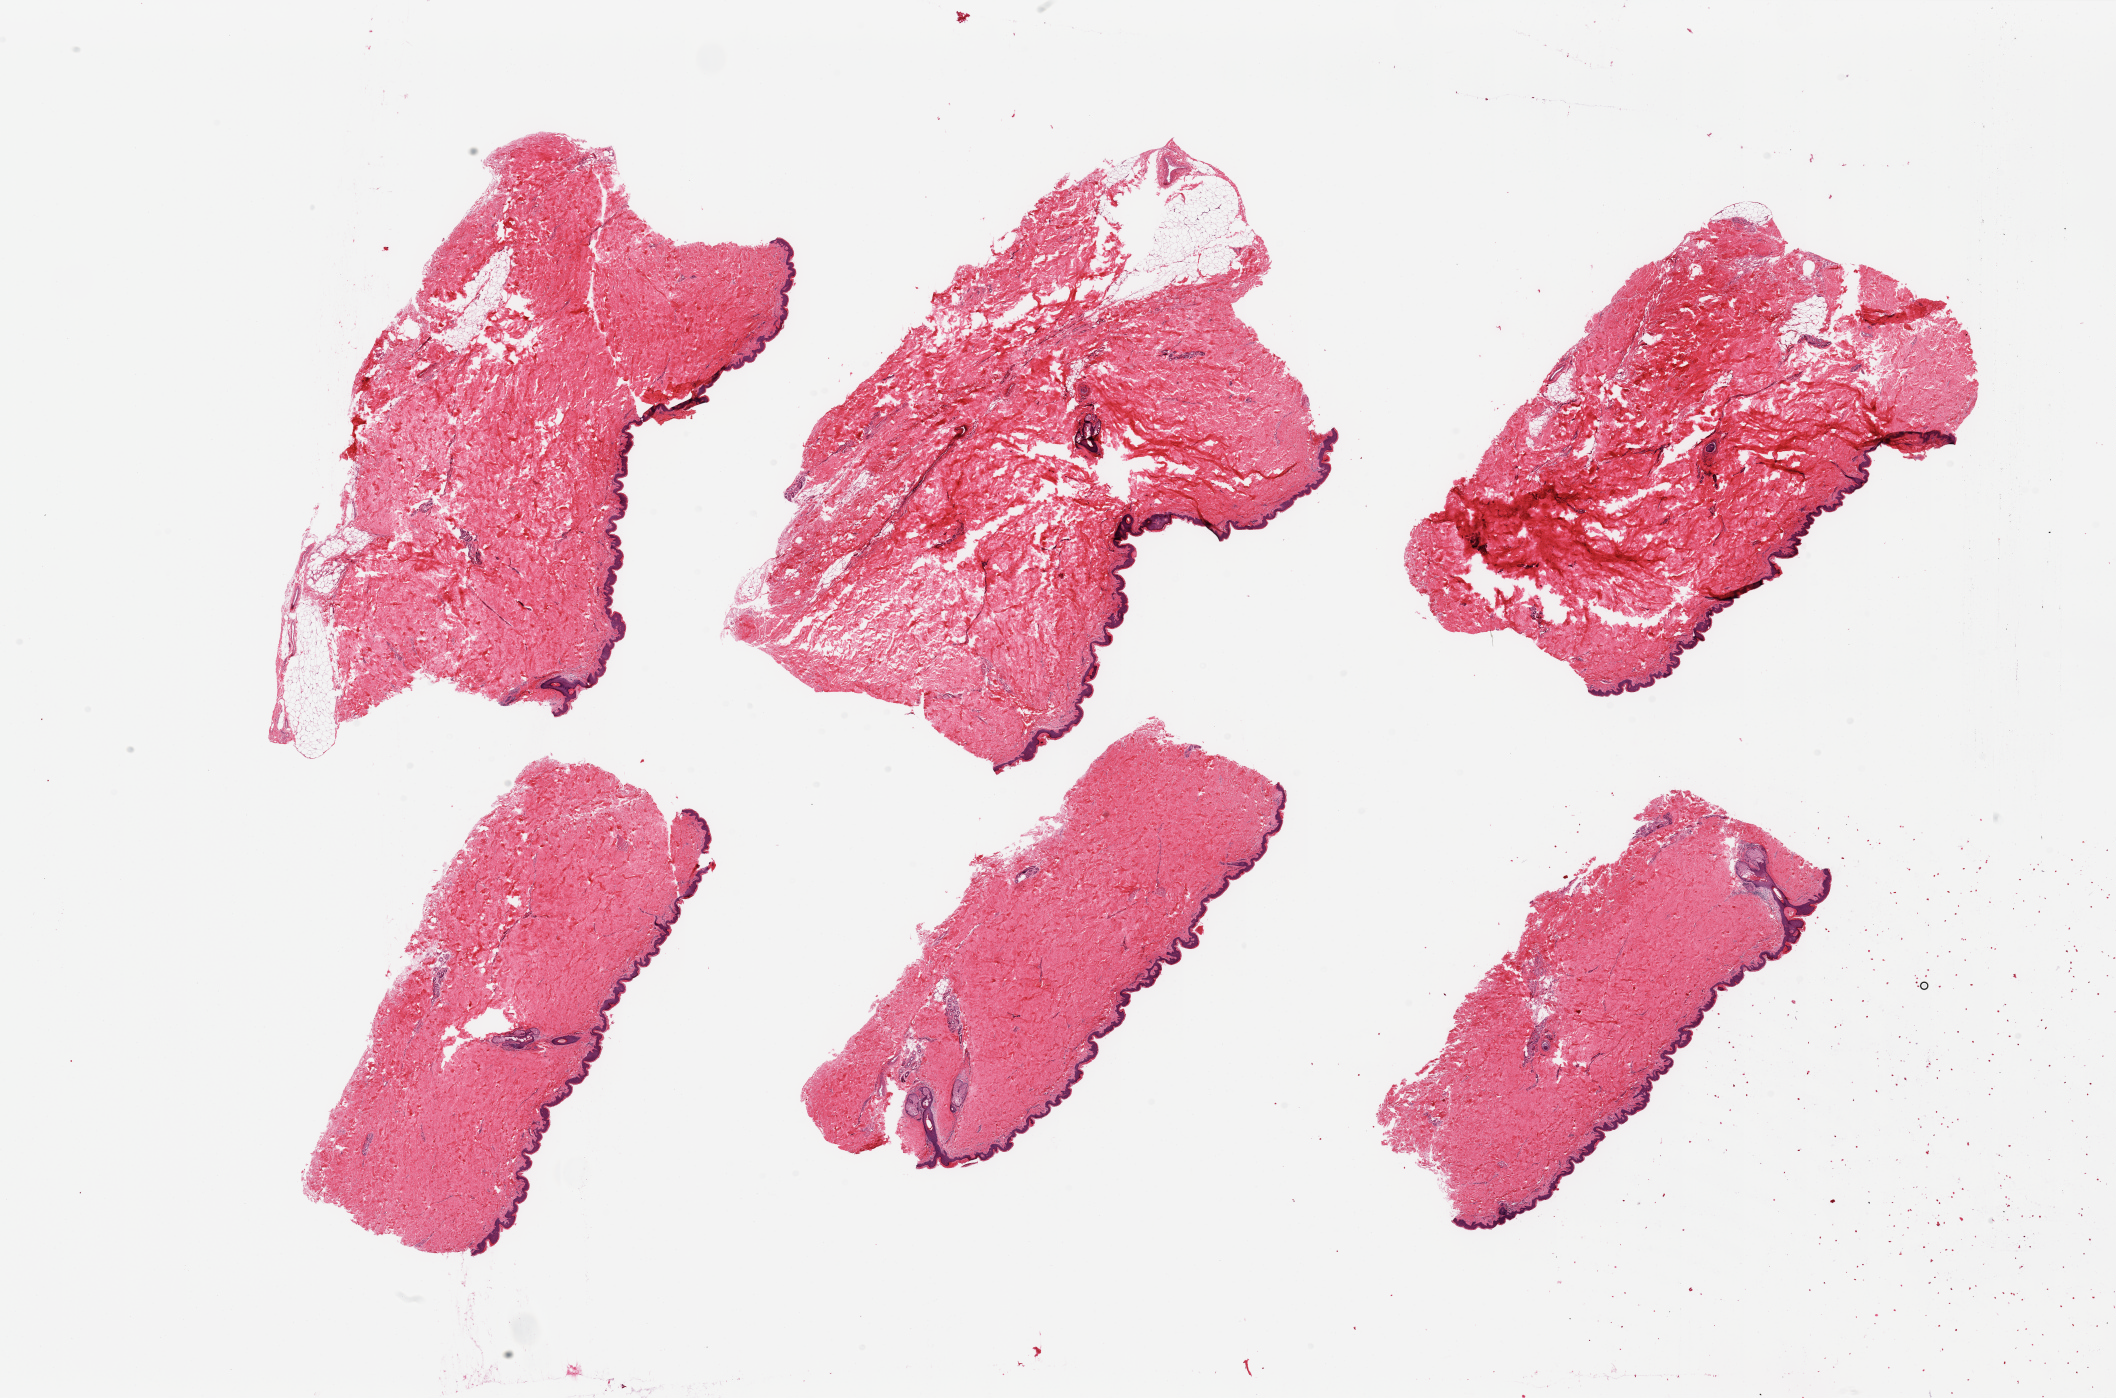
Digitized H&E-stained section, shown as a low-resolution overview of the whole scanned area (about 33.5 x 22.1 mm), PAXgene-fixed paraffin-embedded (PFPE) section, sampled site (target tissue): skin of suprapubic region, donor tissue sample. Male donor.
• reviewer comment on this tissue sample: 6 pieces; 10% dermal fat; well trimmed